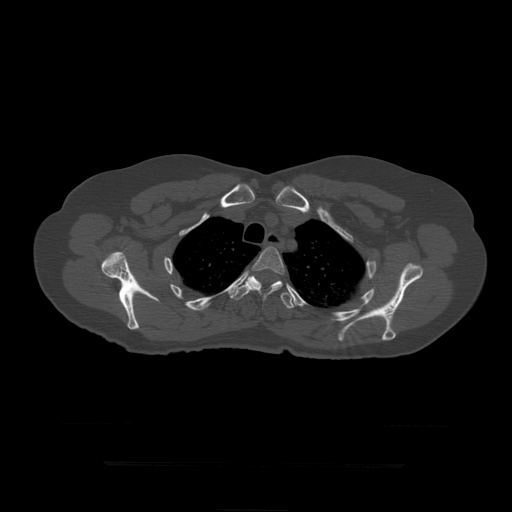
CT including the spine, one axial slice. Position 344 of 399 along the scan axis. Reconstruction kernel STANDARD. 120 kVp. Bone window (W 1800 / L 400 HU). 512 × 512 image matrix. Patient age 41 years. Case-level facts recorded for this patient, not image findings: primary cancer: breast.
Outlined on this slice (semi-automatic segmentation, software-assisted and operator-edited):
- T4 vertebra: bounding box <246,247,285,302> (left, top, right, bottom; pixels)
- T5 vertebra: <228,276,295,309>